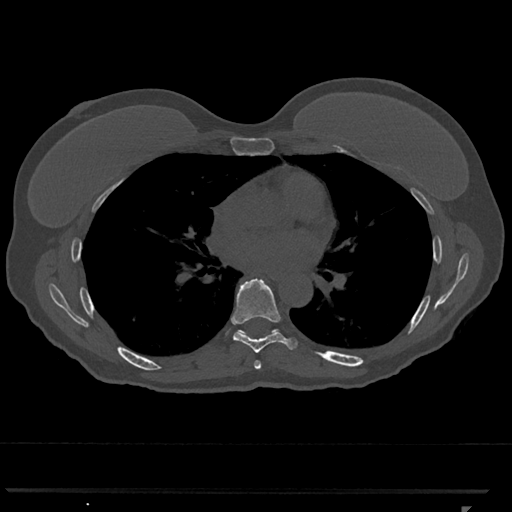
CT including the spine, one axial slice. Slice 707 of 793 in the series (ordered by position). Reconstruction kernel Br40s/3. Bone window (W 1800 / L 400 HU). 0.5 mm slice thickness. 512 × 512 image matrix, field of view 380 × 380 mm. Patient: female, 62 years. From the clinical record (not read from this slice): primary cancer: renal.
Outlined on this slice (semi-automatically segmented with operator editing):
- T6 vertebra: box from (x=254, y=361) to (x=262, y=370) px
- T7 vertebra: (x=231, y=279)–(x=299, y=353)